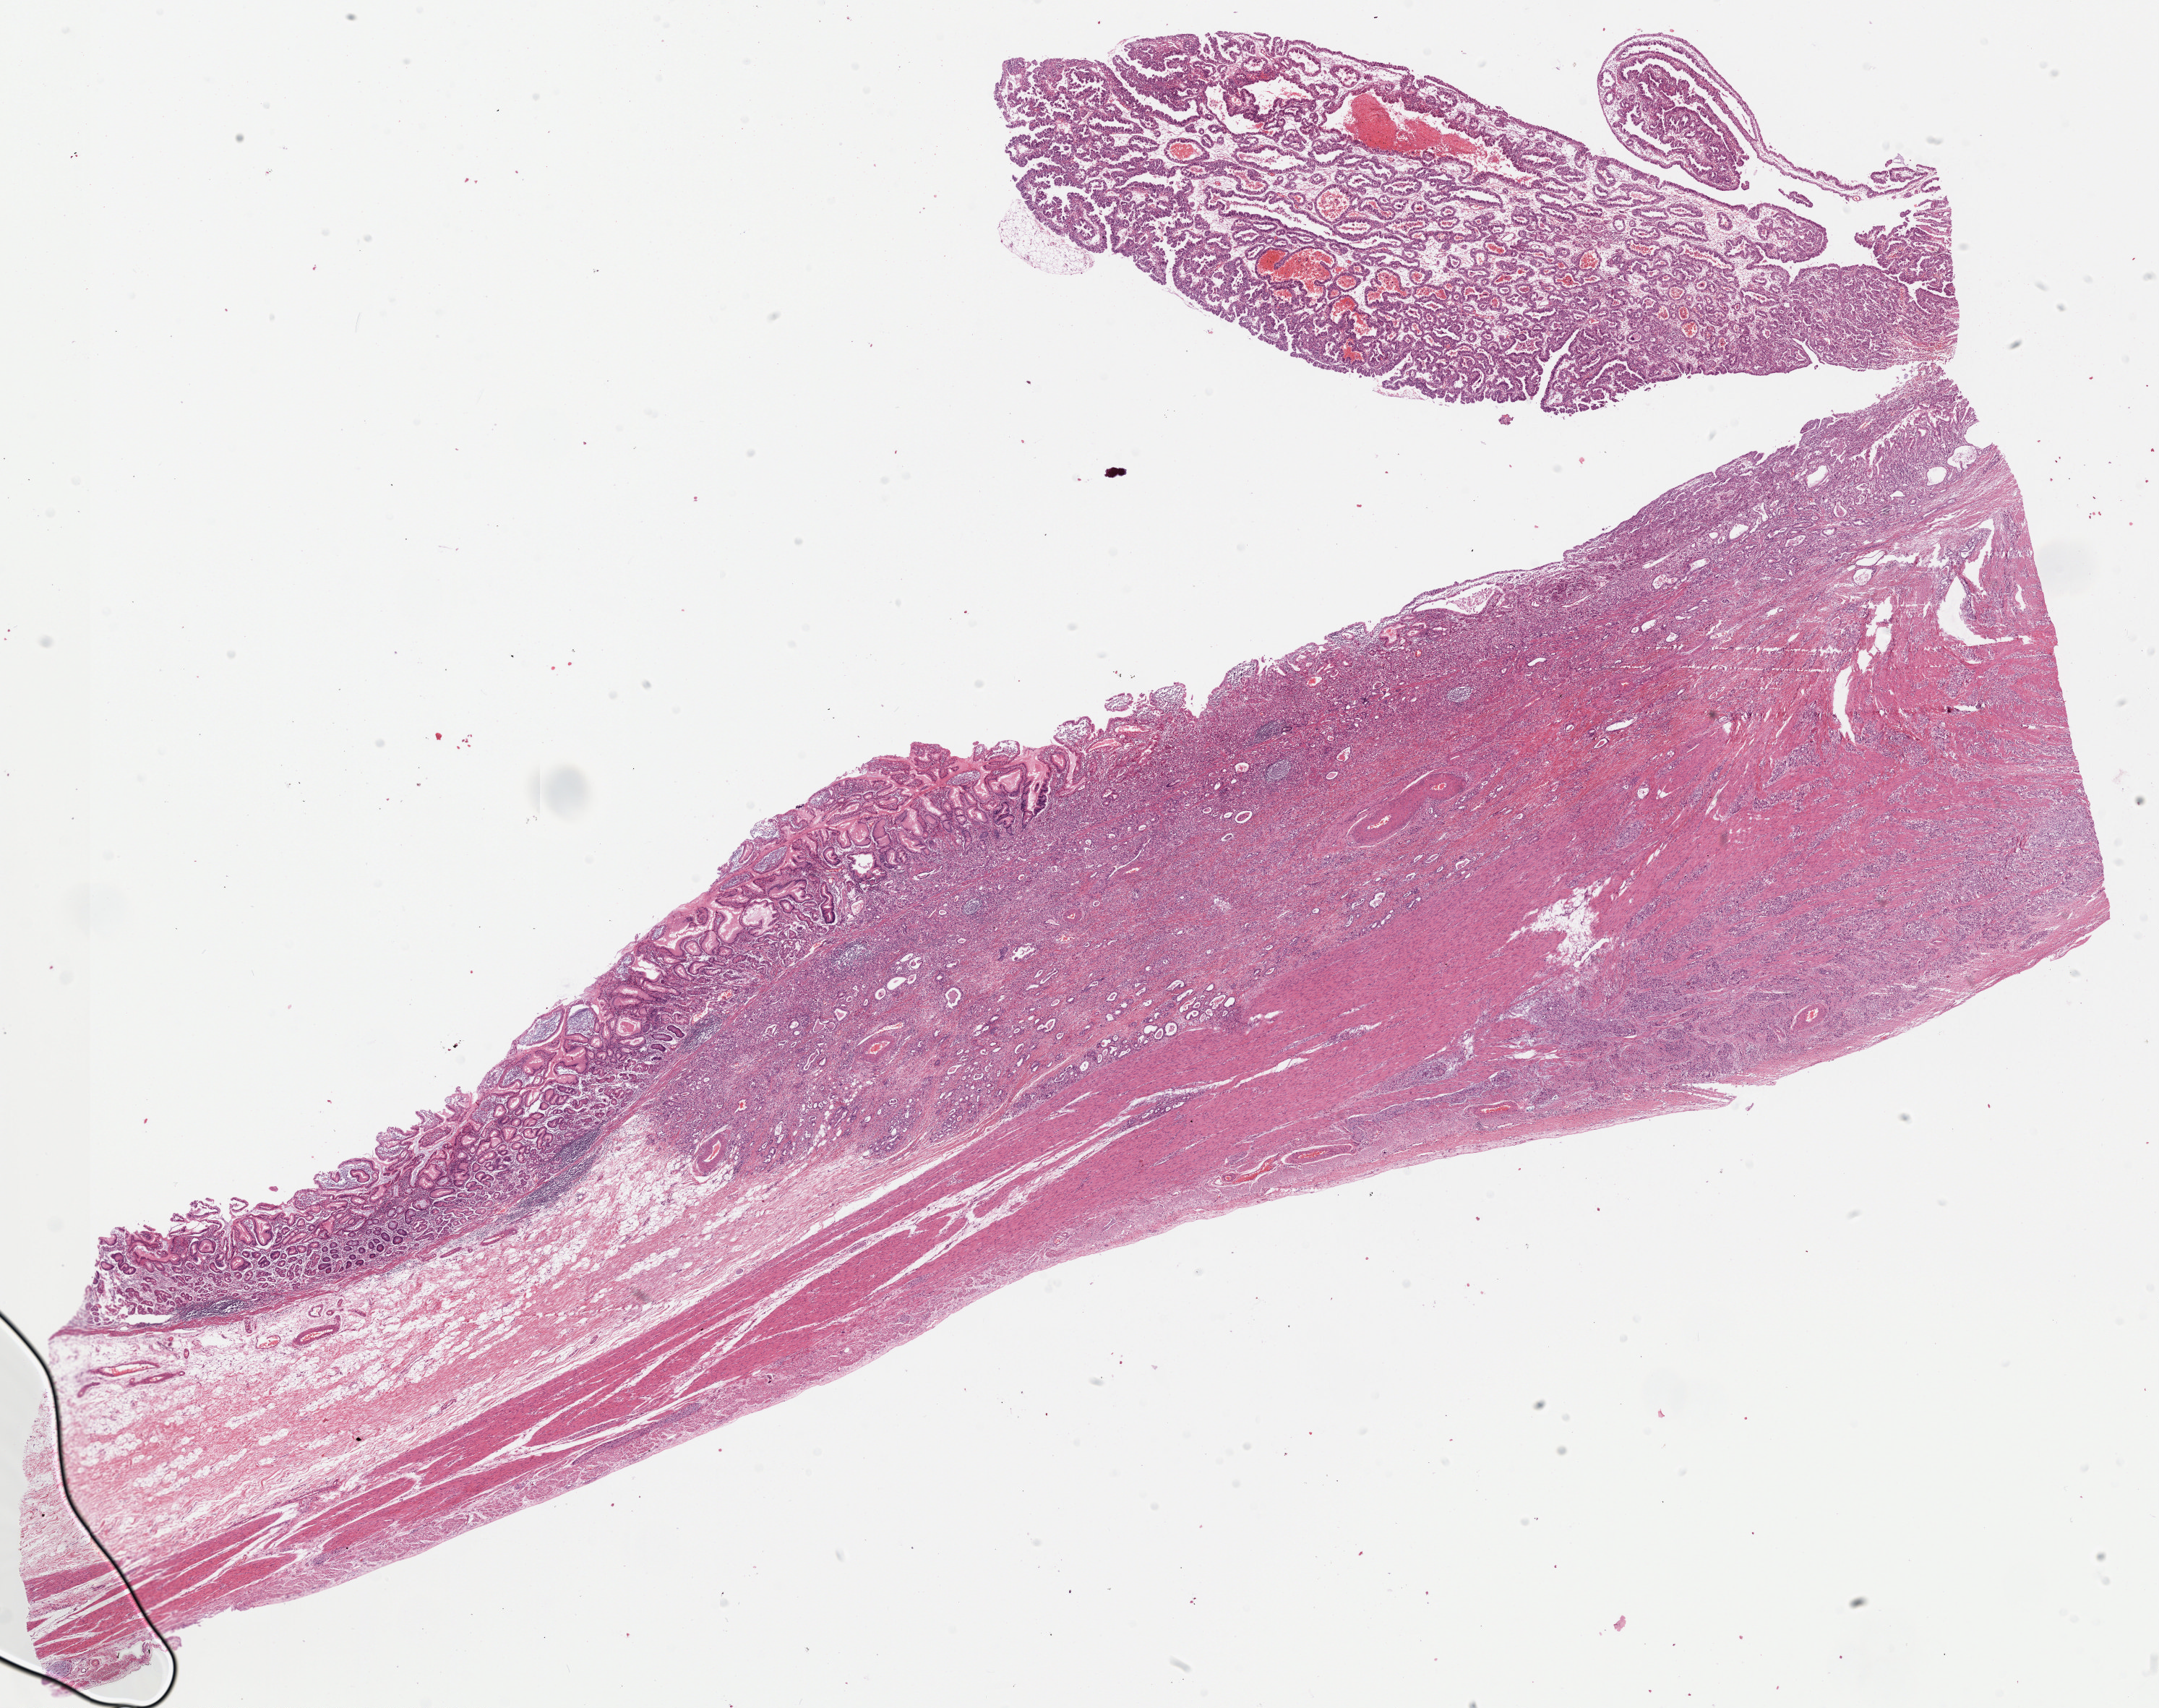
Digitized H&E tissue section (whole slide), a low-resolution overview of the entire scanned area, about 23.6 x 18.7 mm; formalin-fixed paraffin-embedded (FFPE) diagnostic section; sample: primary tumour, stomach. Male patient; age at initial diagnosis 72 years. Histologic grade: G3 (poorly differentiated).
• lymph nodes positive (case pathology): 0 of 60 examined
• histologic diagnosis: Papillary adenocarcinoma, NOS (body of stomach)
• AJCC pathologic stage: IIA (7th edition)